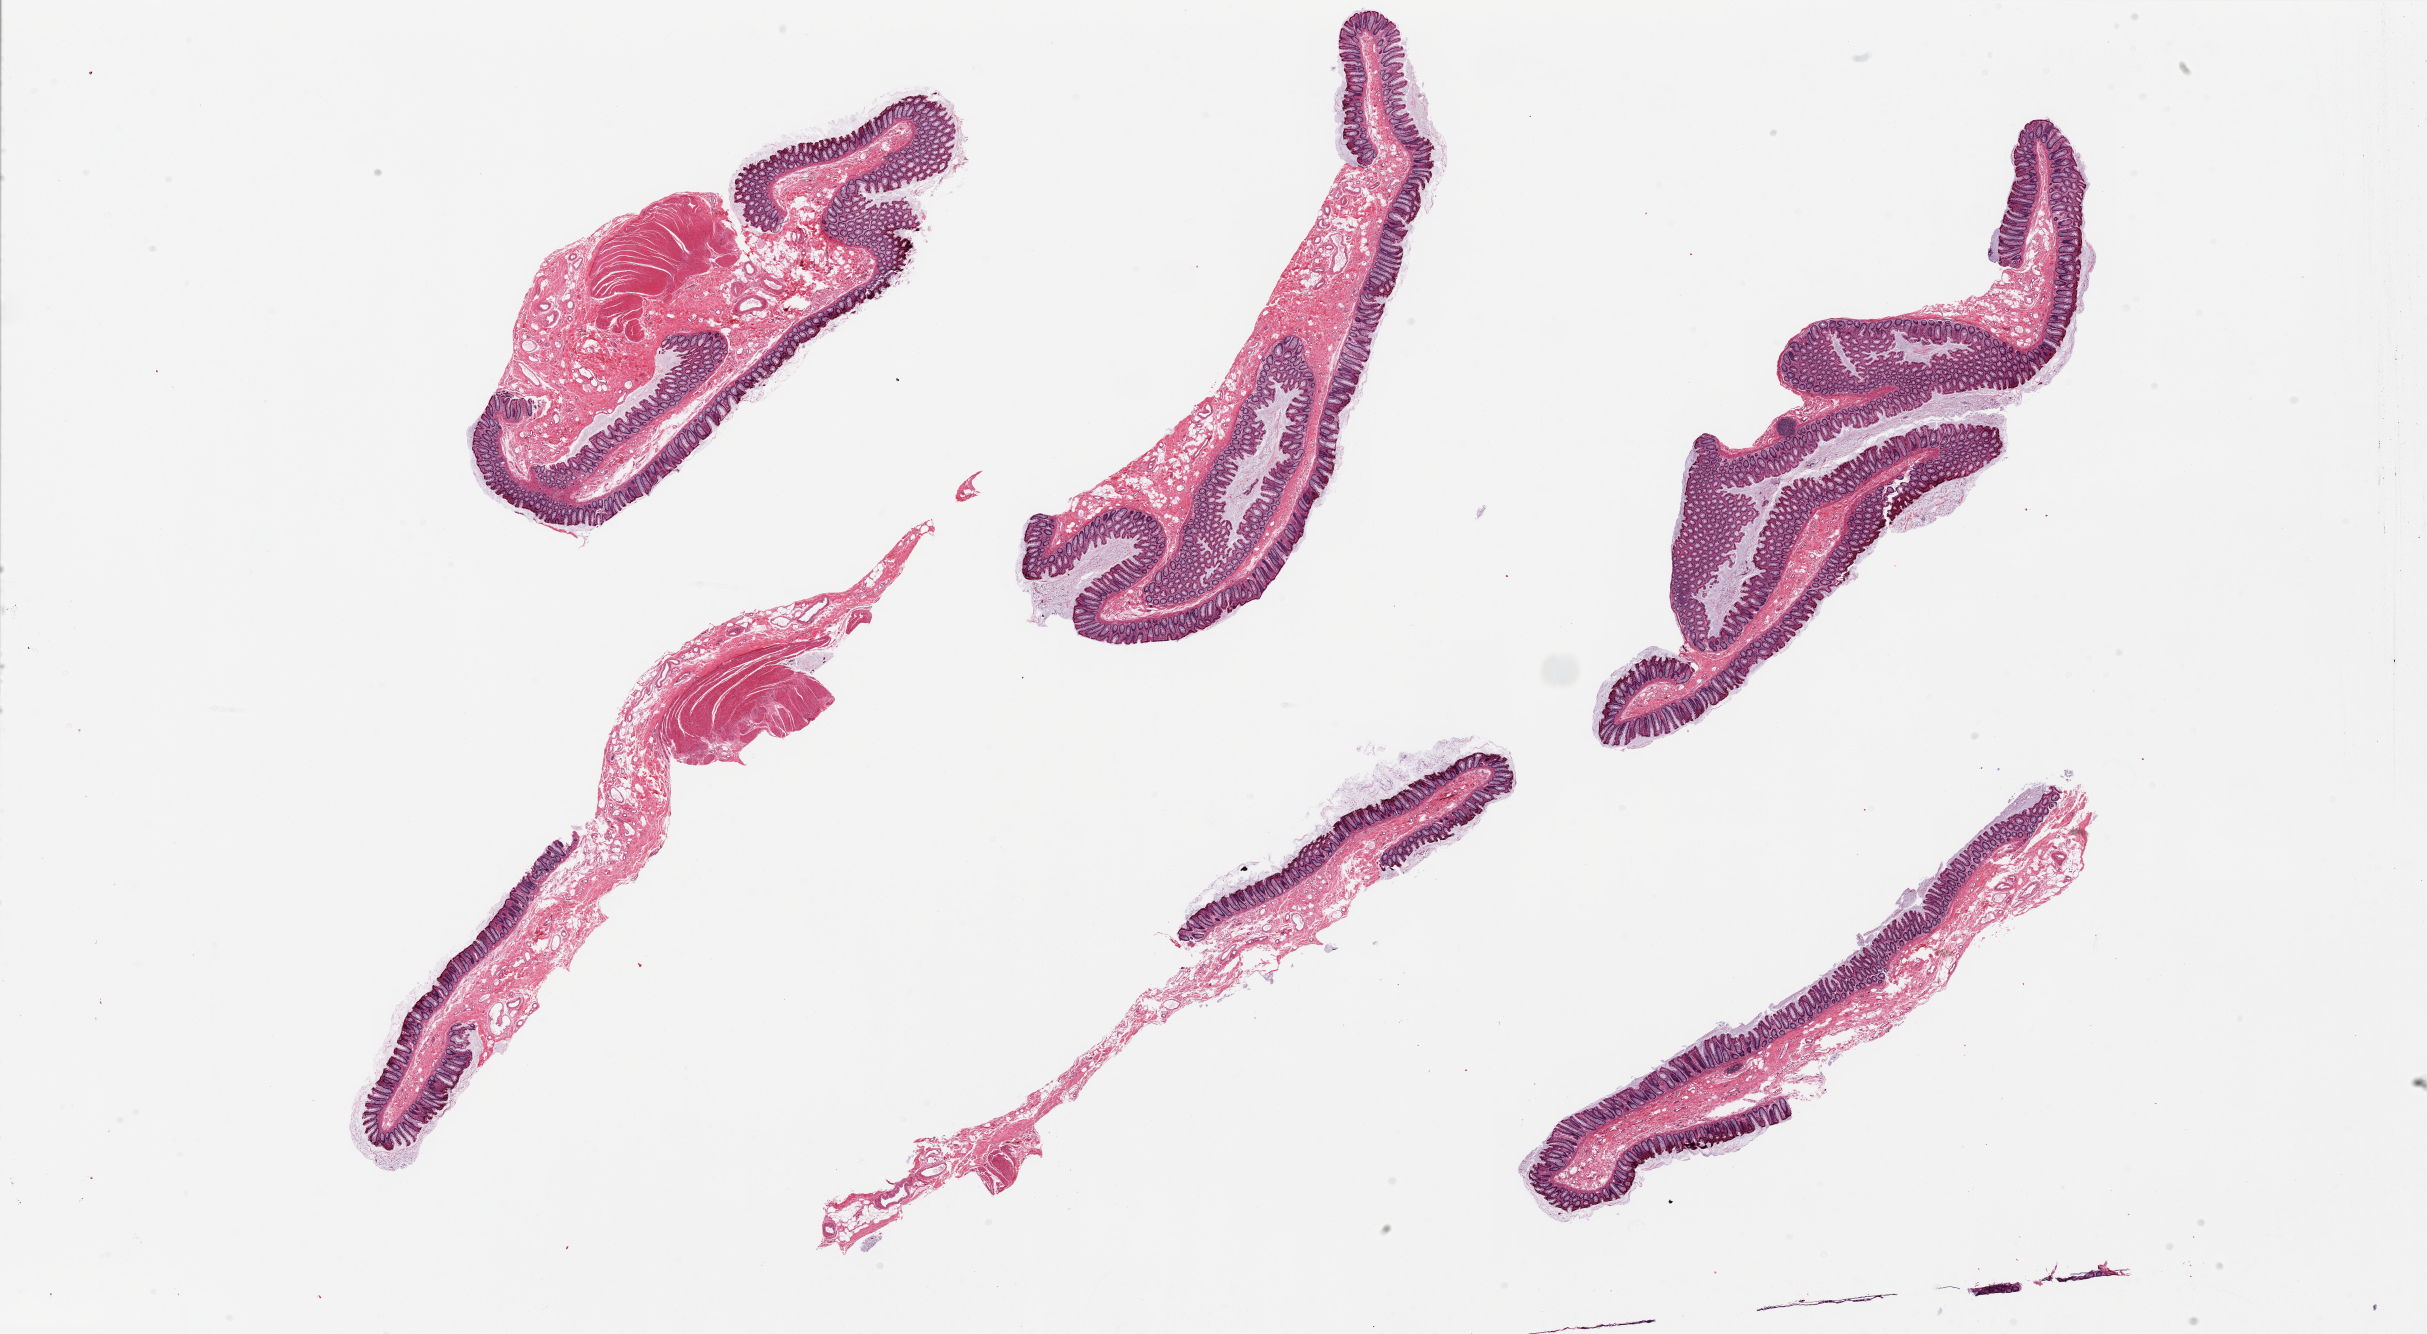
Whole-slide image, haematoxylin and eosin stain — a low-resolution overview of the entire scanned area, about 38.4 x 21.1 mm, PAXgene-fixed paraffin-embedded (PFPE) section, sampled site (target tissue): transverse colon, donor tissue sample. Female donor.
Review note (as recorded): 6 pieces, predominantly mucosa and submucosa, few with attached portion of muscularis.